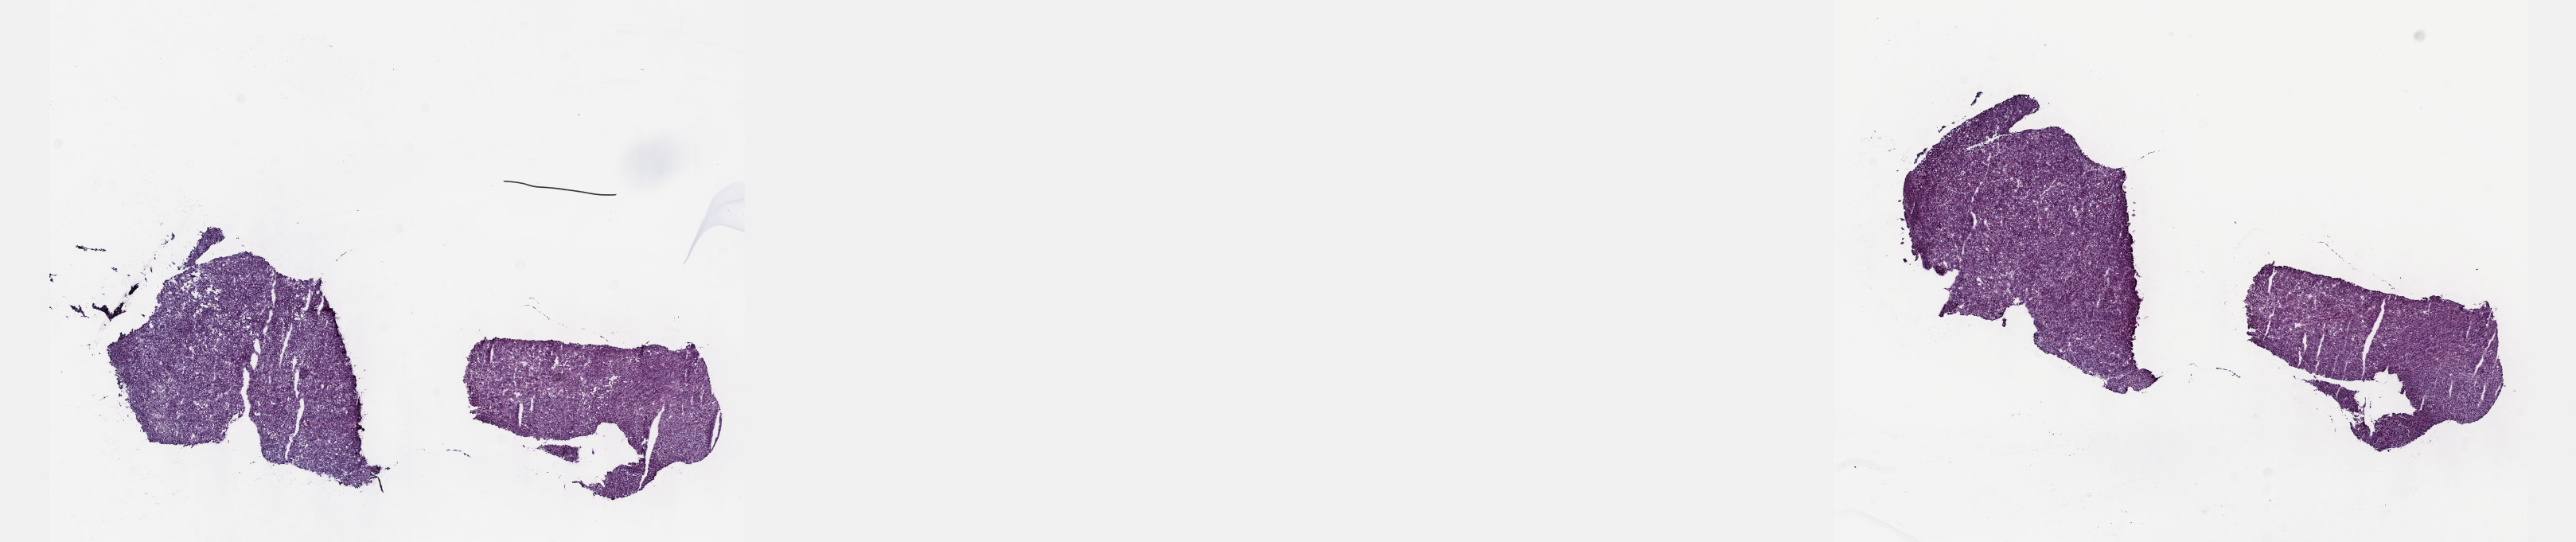
Digitized H&E tissue section (whole slide), low-resolution overview of the scanned area, about 26.2 x 5.5 mm (slide scanned at 40x), frozen section, liver, primary tumour sample. Patient: male, age at initial diagnosis 69 years. Histologic grade: G3 (poorly differentiated). Pathologist review of this section (percent, as recorded): tumour cells 97%, tumour nuclei 98%, normal cells 0%, stromal cells 2%, necrosis 1%. Inflammatory infiltration, as recorded: lymphocyte infiltration 1%, monocyte infiltration 0%, neutrophil infiltration 0%.
AJCC pathologic stage: I (7th edition). TNM: T1 N0 M0. Pathologic diagnosis: Hepatocellular carcinoma, NOS.